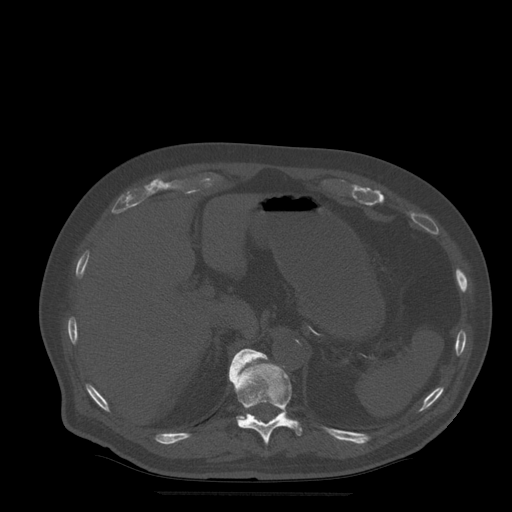
CT including the spine, one axial slice. Position 241 of 522 along the scan axis. Bone window (W 1800 / L 400 HU). 1.25 mm slice thickness. 512 × 512 image matrix, field of view 420 × 420 mm. Patient age 72 years. Case-level facts recorded for this patient, not image findings: primary cancer: prostate.
Outlined on this slice (semi-automatically segmented with operator editing):
- T11 vertebra: bounding box [x1, y1, x2, y2] px = [229, 349, 303, 445]
- T12 vertebra: [230, 350, 259, 419]